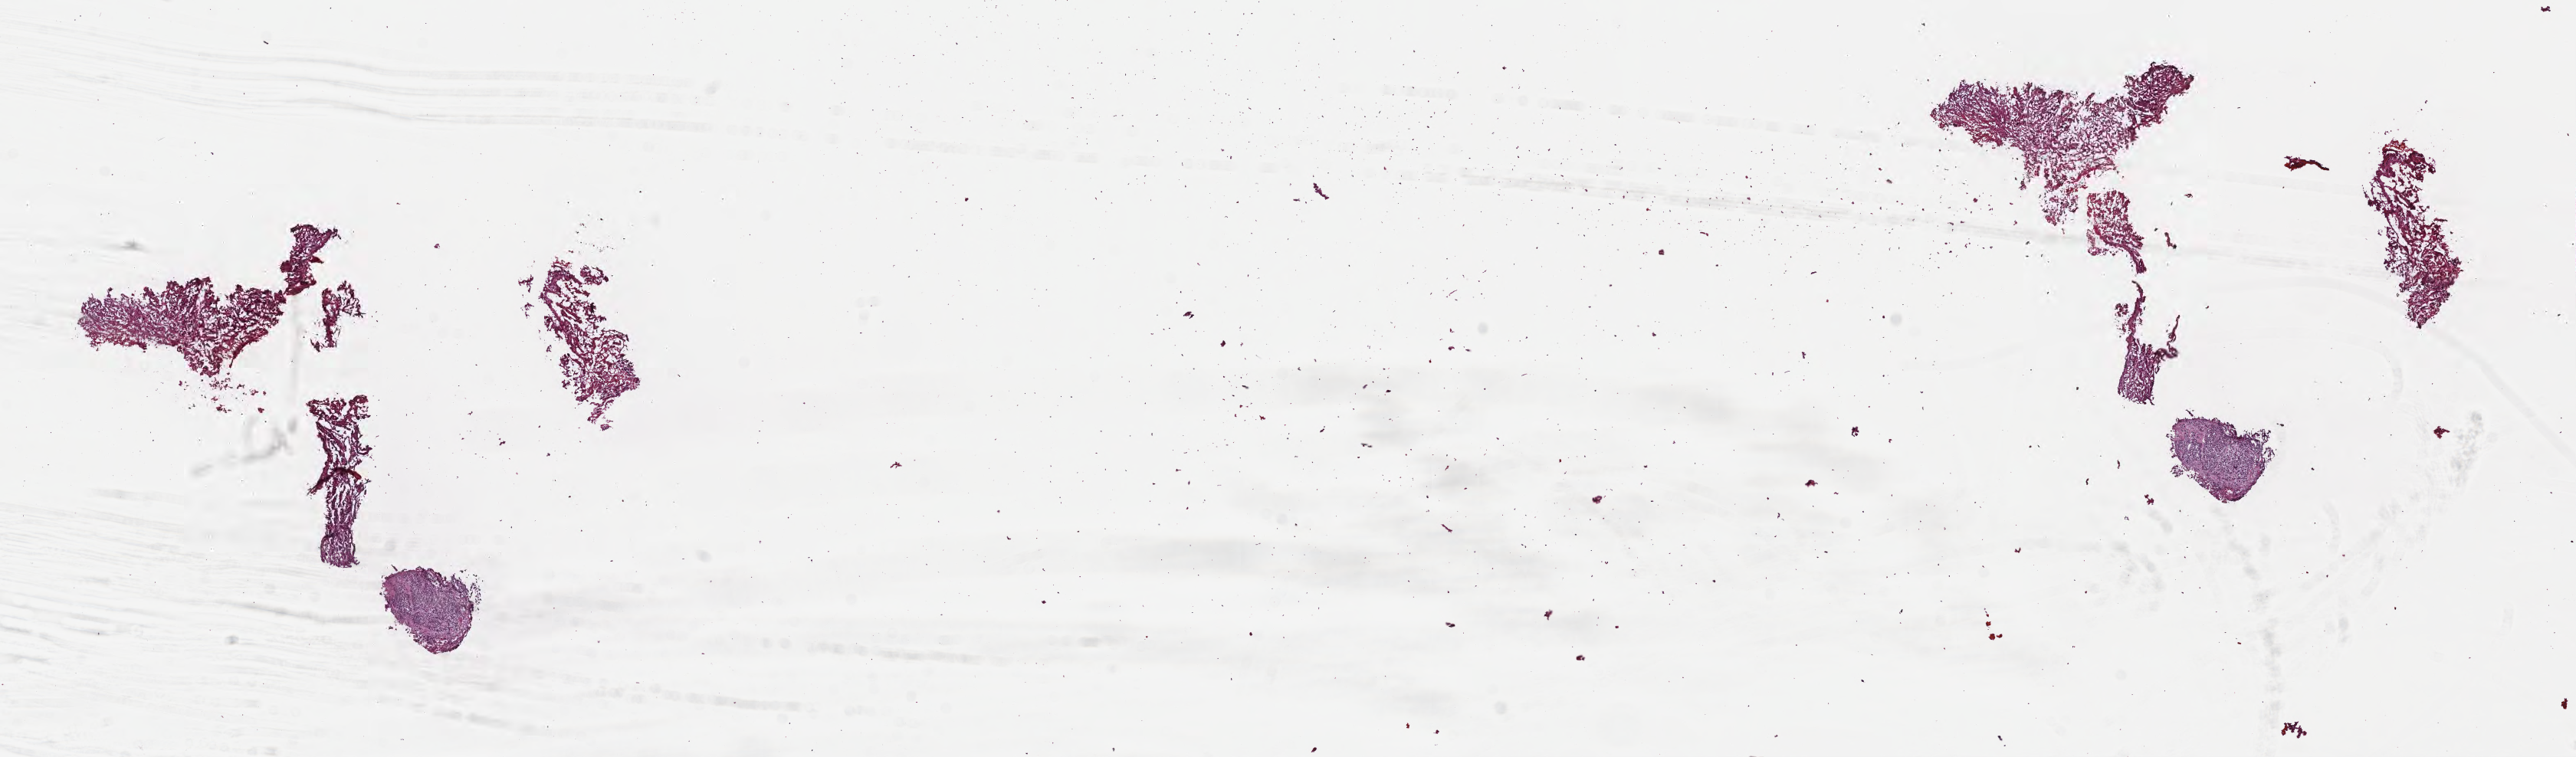
Whole-slide image, haematoxylin and eosin stain — low-resolution overview of the scanned area, about 27.2 x 8.0 mm; frozen section (tissue freezing medium); metastatic tumor tissue, resected from brain. Male patient; age at initial diagnosis 65 years. Pathologist review of this section (percent, as recorded): tumor cells 40%, tumor nuclei 50%, stromal cells 20%, necrosis 0%, normal cells 40%. Inflammatory infiltration, as recorded: lymphocyte infiltration 0%, monocyte infiltration 0%, neutrophil infiltration 0%.
• patient diagnosis (primary): Small cell carcinoma, NOS